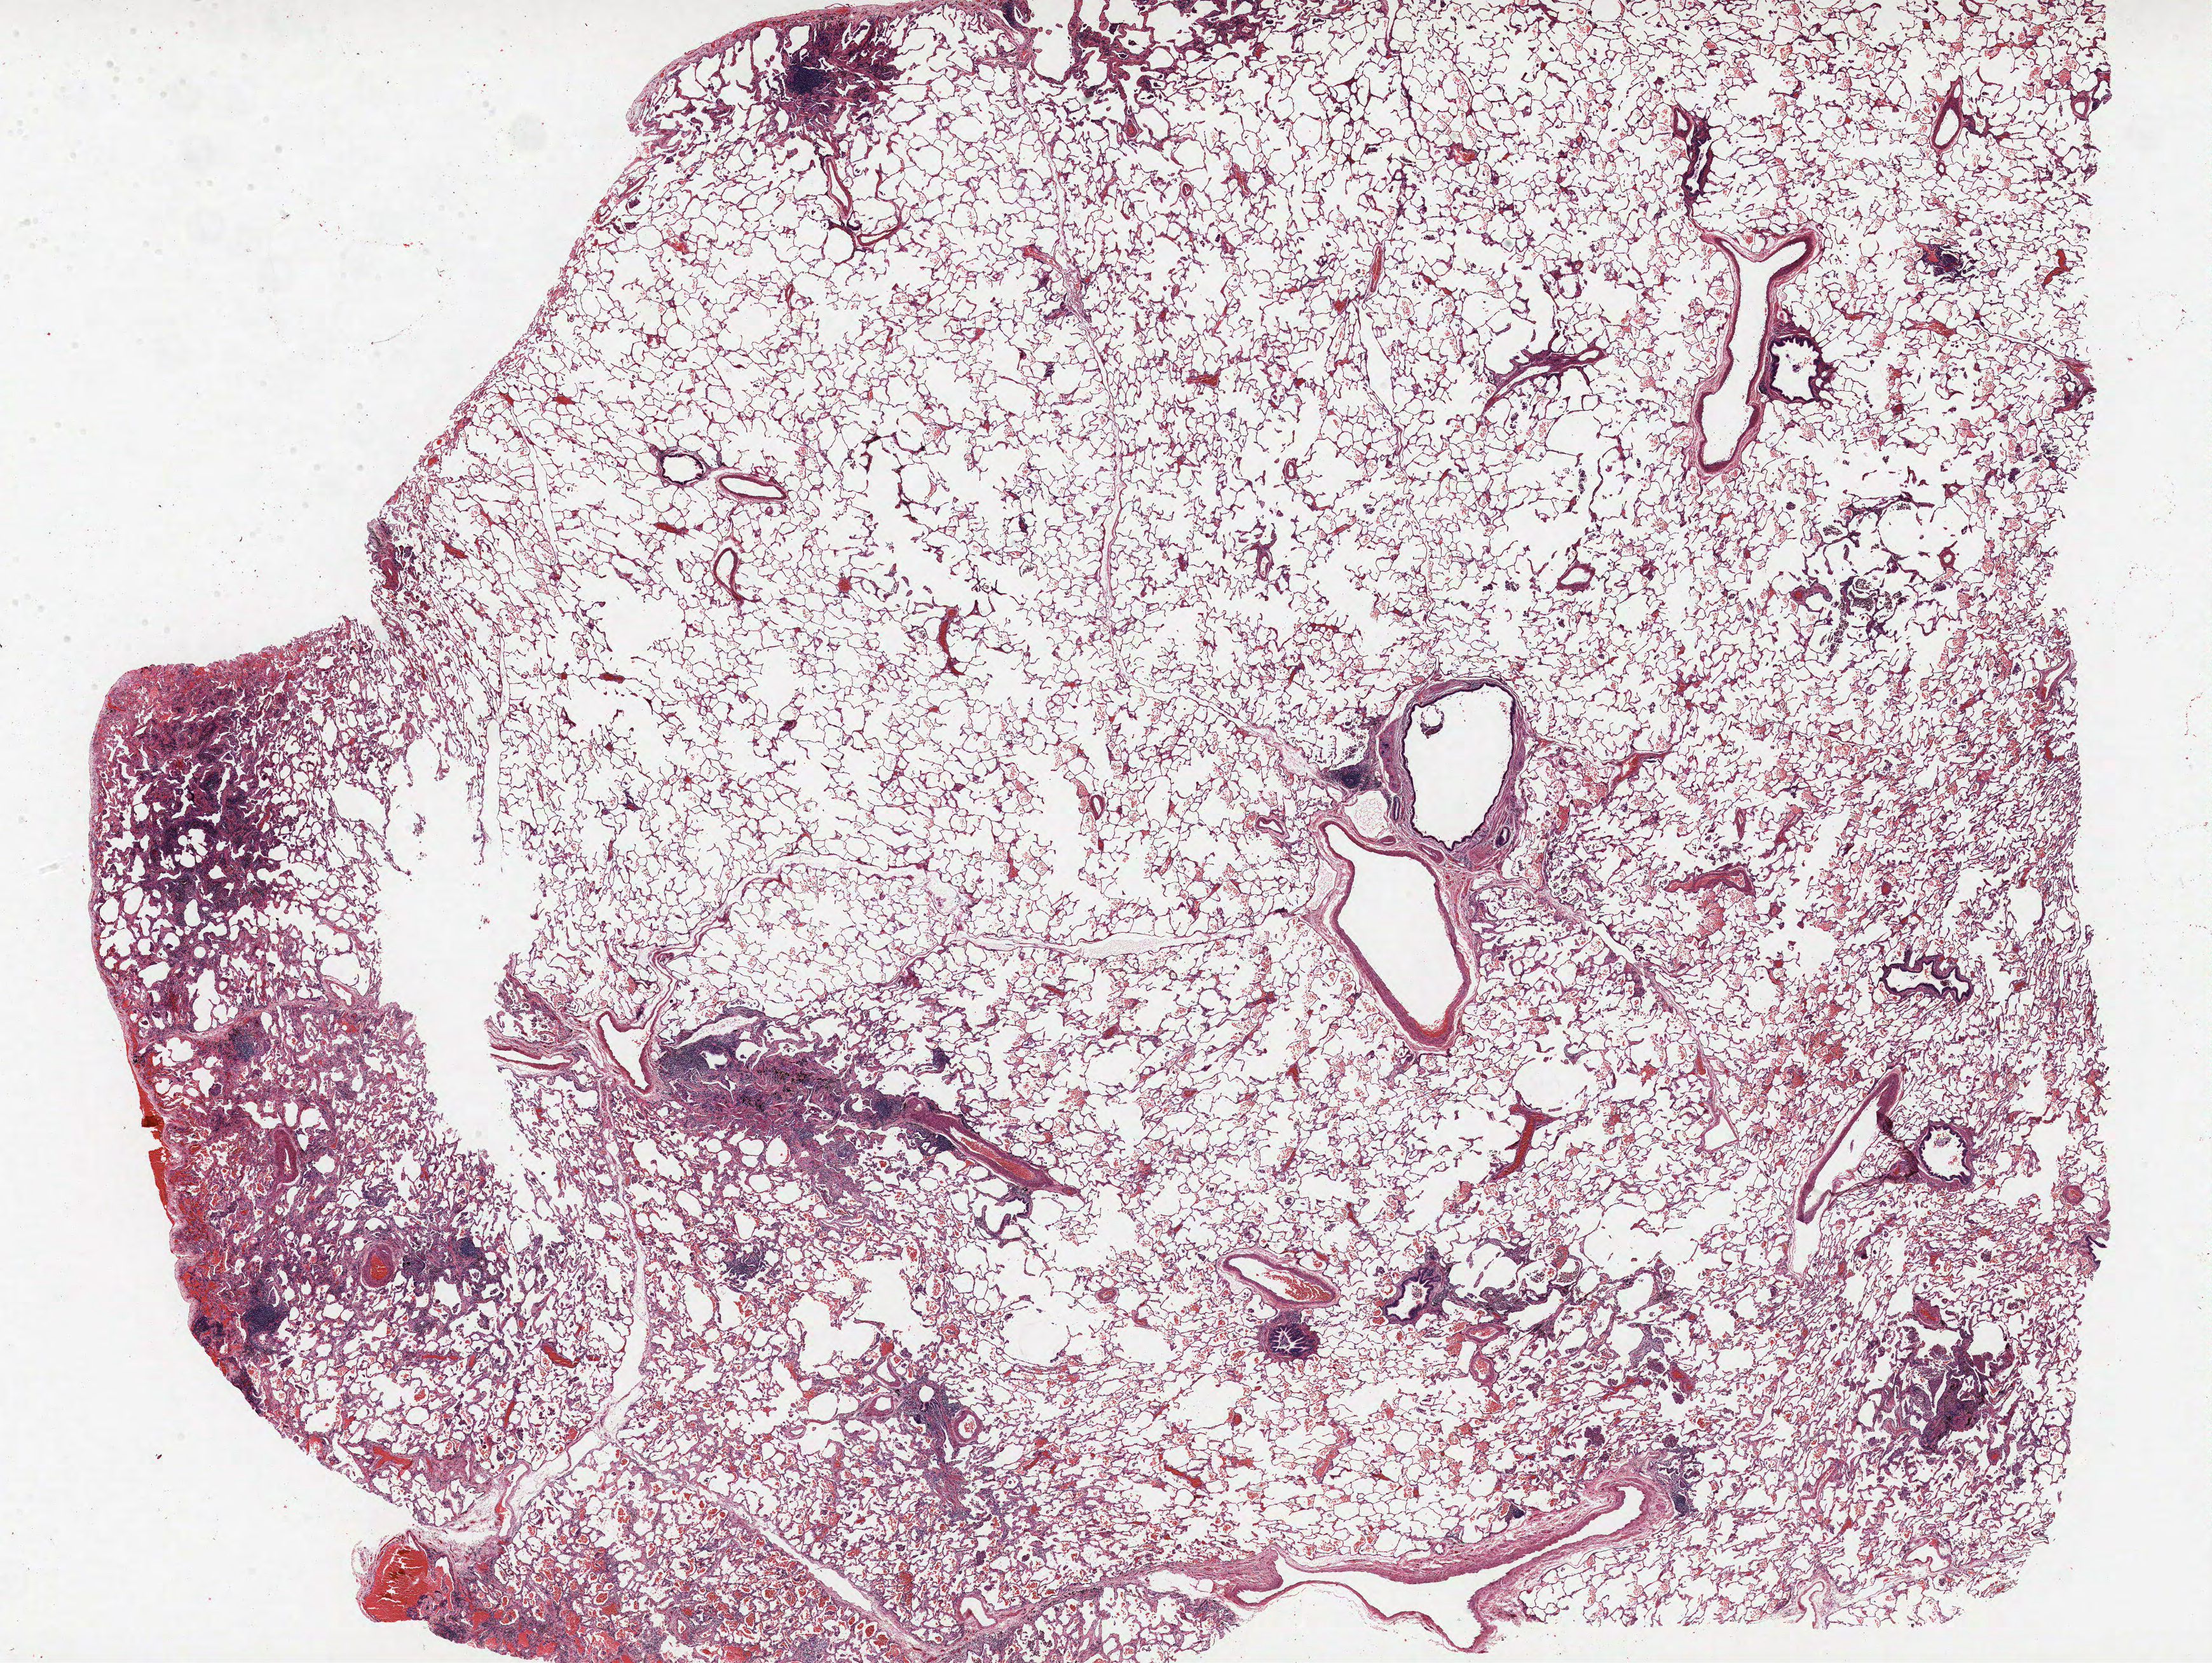
Whole-slide histology image, Hematoxylin and eosin (H&E) stained — low-resolution overview of the scanned area, about 27.8 x 20.9 mm (slide scanned at 40x); FFPE section; lung. Male, age 57 at enrolment. Current smoker at enrolment. Grade: moderately differentiated (G2).
Tumour size (pathology): 18 mm. Primary tumour location (clinical record): right middle lobe. Stage (AJCC 6th edition): IB. Participant's lung-cancer diagnosis: Squamous cell carcinoma, NOS. Note: participant had 2 primary lung cancers recorded; fields above describe the first.